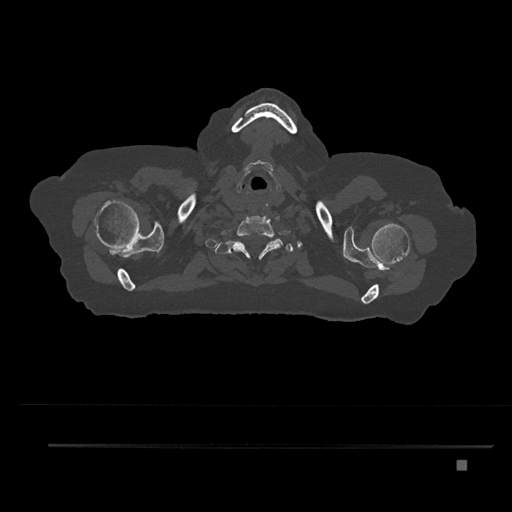
CT including the spine, one axial slice. Reconstruction kernel Br40s/3. 120 kVp. Bone window (W 1800 / L 400 HU). 512 × 512 image matrix. Patient: female, 76 years. From the clinical record (not read from this slice): primary cancer: lung; vertebrae with lytic lesions (as recorded): T11, L3.
Annotated regions visible in this slice (semi-automatic segmentation, software-assisted and operator-edited):
- T1 vertebra: bounding box <222,239,276,258> (left, top, right, bottom; pixels)